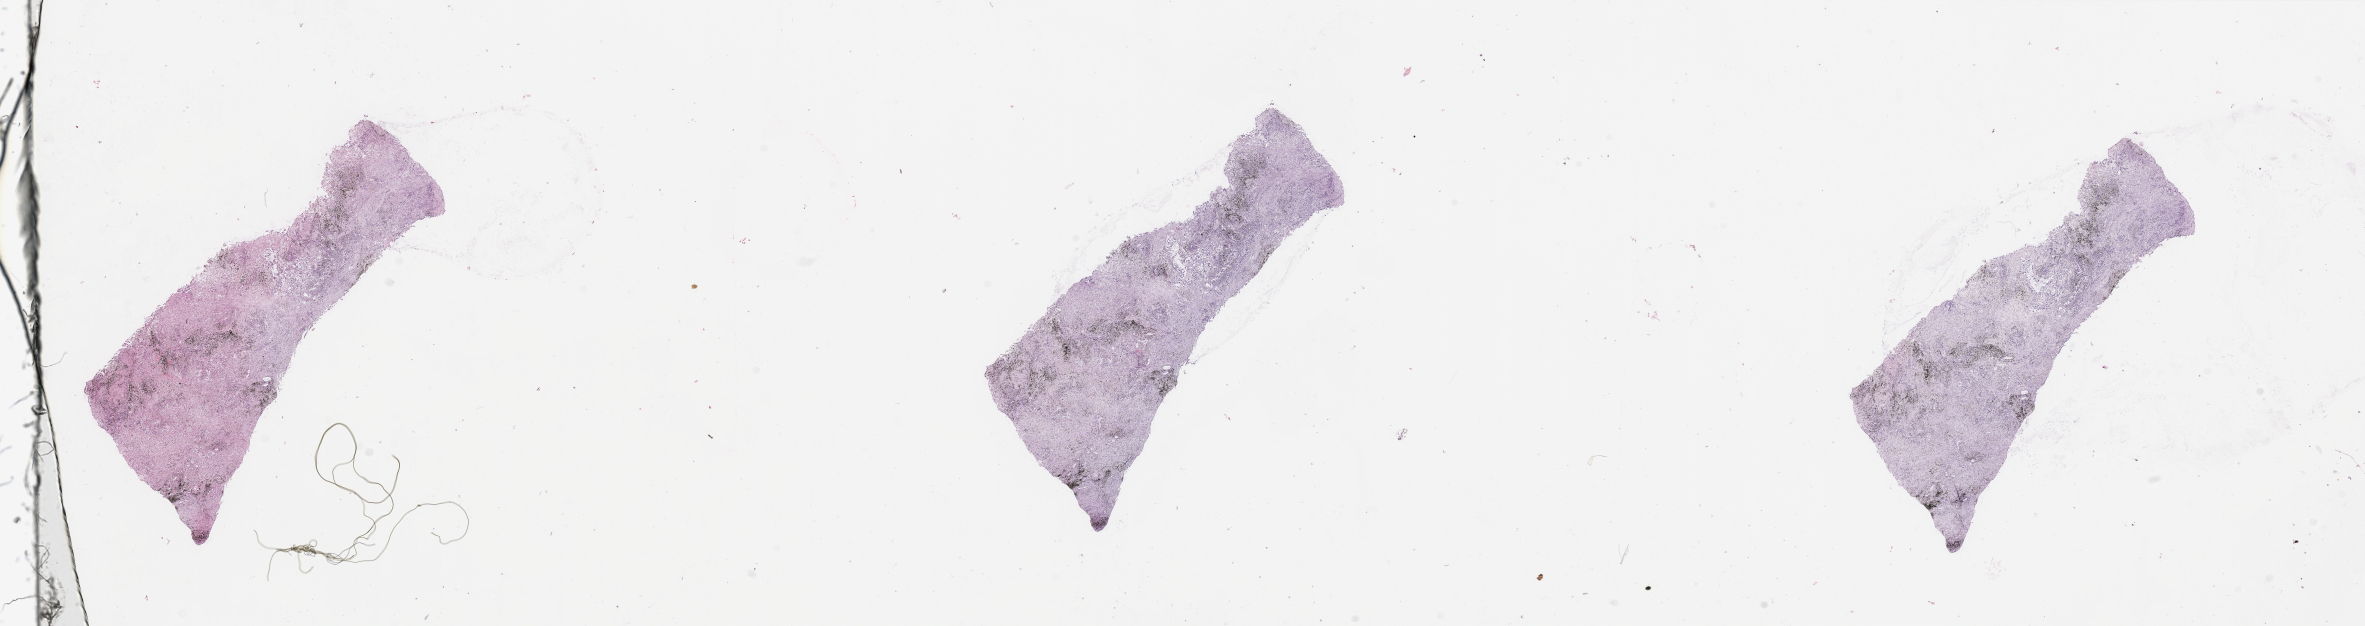
H&E whole-slide image — shown as a low-resolution overview of the whole scanned area (about 37.4 x 9.9 mm). Lung, tumour tissue. 76-year-old male patient. Histologic grade: G2 (moderately differentiated).
- AJCC pathologic stage: IIA
- diagnosis: Adenocarcinoma, NOS